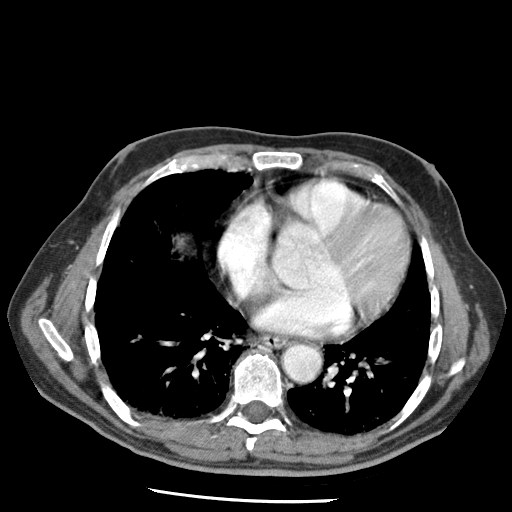
Contrast-enhanced abdominal CT (liver protocol), one axial slice; reconstruction kernel STANDARD; 120 kVp; soft-tissue window (W 400 / L 40 HU); 512 × 512 image matrix, field of view 320 × 320 mm. From the clinical record (not read from this slice): diagnosis: hepatocellular carcinoma (patient treated with transarterial chemoembolisation; whether this scan precedes or follows treatment is not stated here); TNM stage (as recorded): Stage-IIIA; Child-Pugh class: A; tumour differentiation: moderately differentiated; tumour nodularity: multinodular.
Annotated regions visible in this slice (semi-automatically segmented with operator editing):
- liver parenchyma outside the tumour (the mass and vessels are separate outlines, so this box may not span the whole liver): bounding box (x1, y1, x2, y2) in pixels: (178, 238, 184, 246)